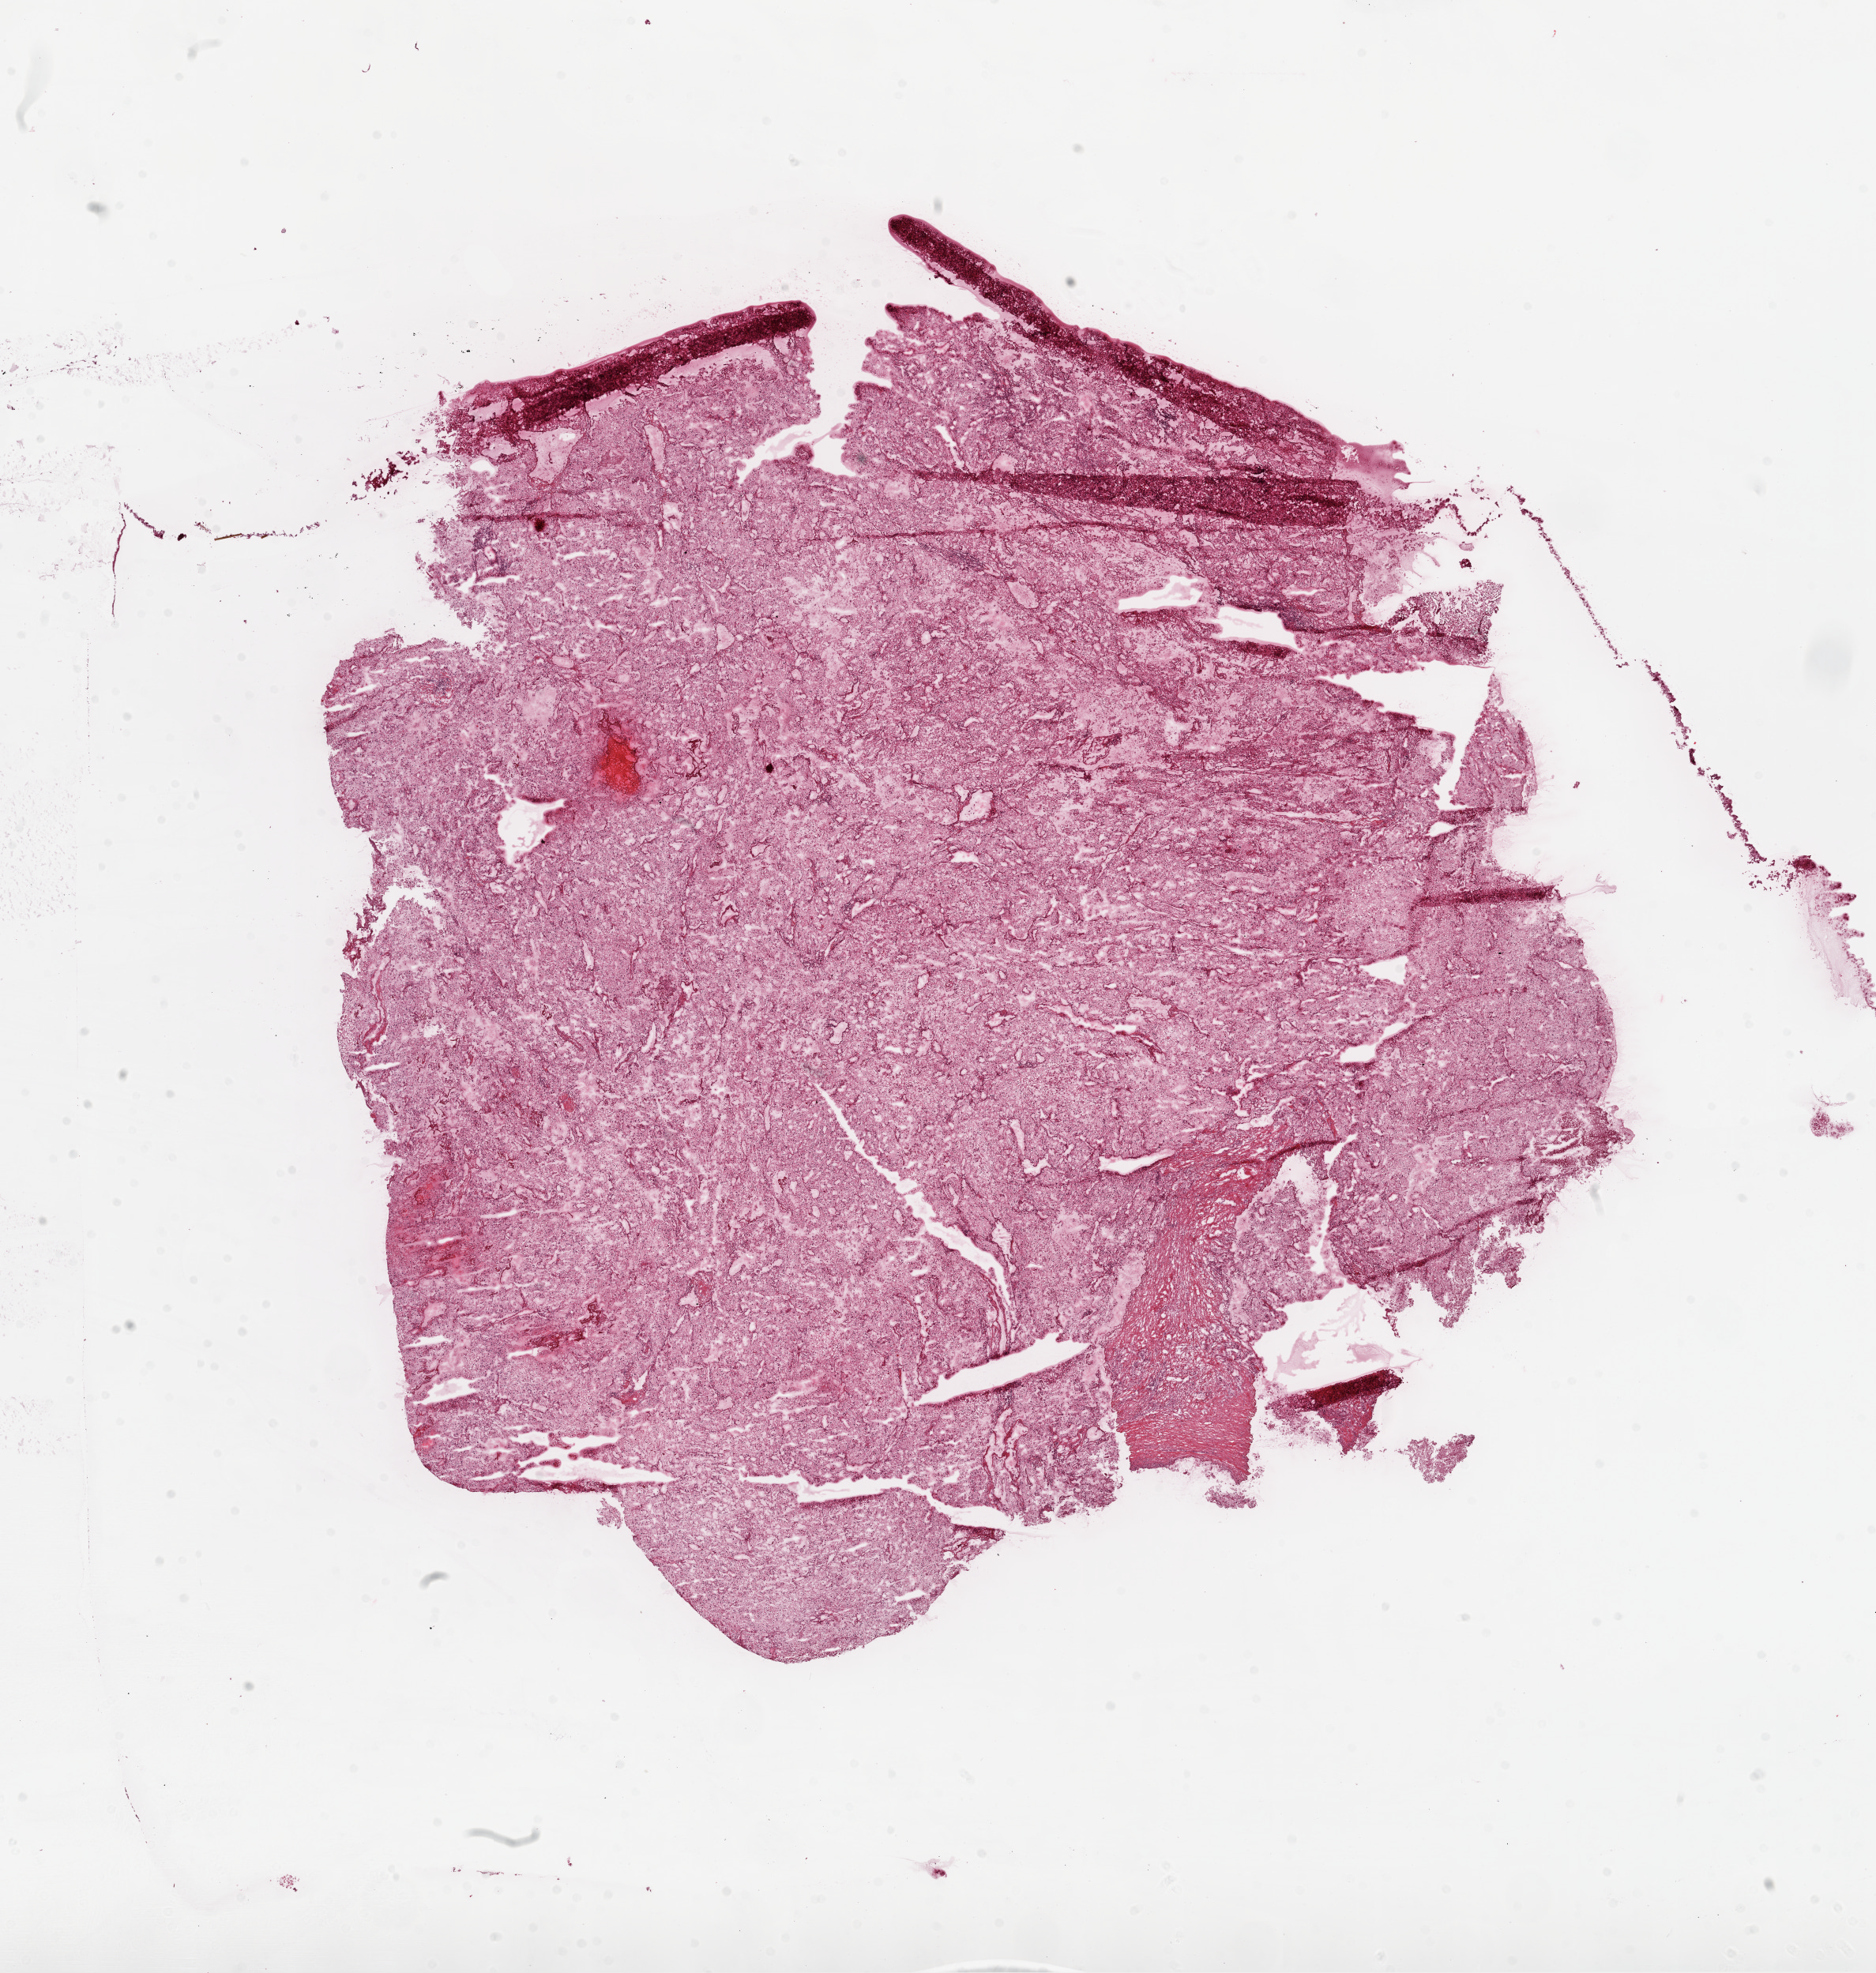
Whole-slide histology image, Hematoxylin and eosin (H&E) stained, low-resolution overview of the scanned area, about 19.1 x 20.0 mm (from a 20x scan). Frozen section from the top of the tissue portion. Kidney, primary tumour sample. Patient: male, age at initial diagnosis 58 years. Histologic grade: G4 (undifferentiated). Pathologist review of this section (percent, as recorded): tumour cells 85%, tumour nuclei 85%, normal cells 0%, stromal cells 15%, necrosis 0%.
Laterality: right. Lymph nodes positive (case pathology): 0 of 7 examined. AJCC pathologic stage: IV. Pathologic diagnosis: Clear cell adenocarcinoma, NOS.